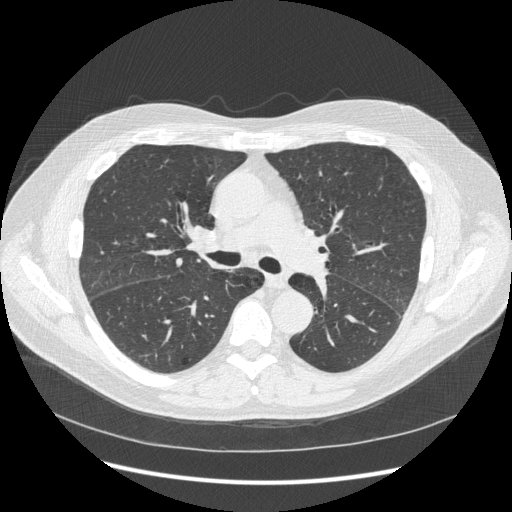
Axial slice from a low-dose chest CT screening exam; second annual screen; lung window (W 1500 / L -600 HU); standard (soft-tissue) reconstruction kernel (STANDARD); slice 111 of 266 in the series; 512 × 512 image matrix. Male participant, aged 59 years at enrolment. Current smoker at enrolment.
Expert-annotated lung lesion, bounding box (x1, y1, x2, y2) in pixels: (179, 216, 235, 257). The exam's reader record, not a measurement of the box and not confirmed to be the same lesion: non-calcified nodule or mass ≥4 mm, lingula, 5 × 5 mm, smooth margins, soft tissue attenuation, pre-existing on the prior screen: yes; interval growth: no. Note: the box lies in the patient's right hemithorax on this image, whereas the reader's record names the left lung; they may be different findings. Lung cancer was diagnosed 540 days after this screen: squamous cell carcinoma, keratinizing, NOS, right hilum, stage IIIB (AJCC 6th edition).